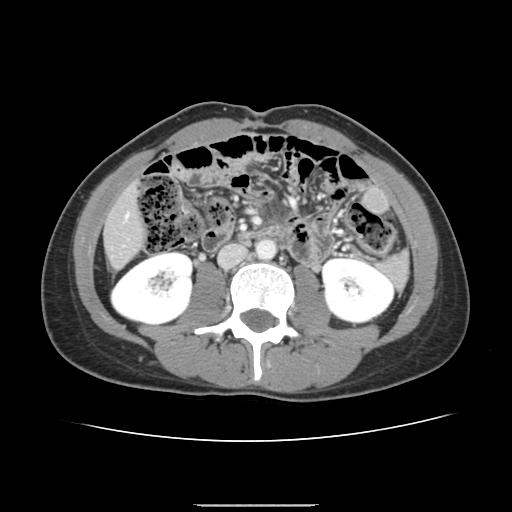
Contrast-enhanced abdominal CT, one axial slice. Position 42 of 150 along the scan axis. Intravenous contrast given. Soft-tissue window (W 400 / L 40 HU). 512 × 512 image matrix, field of view 324 × 324 mm. Female patient, age 32 years. From the clinical record (not read from this slice): diagnosis: colorectal cancer liver metastases, imaged before liver resection; multiple liver metastases: yes; largest metastasis: 0.7 cm; chemotherapy before resection: yes.
Structures marked on this image (outlined manually by an expert reader):
- liver: bounding box (x1, y1, x2, y2) in pixels: (106, 189, 145, 268)
- planned liver remnant (the part of the liver to remain after resection): (106, 188, 144, 268)